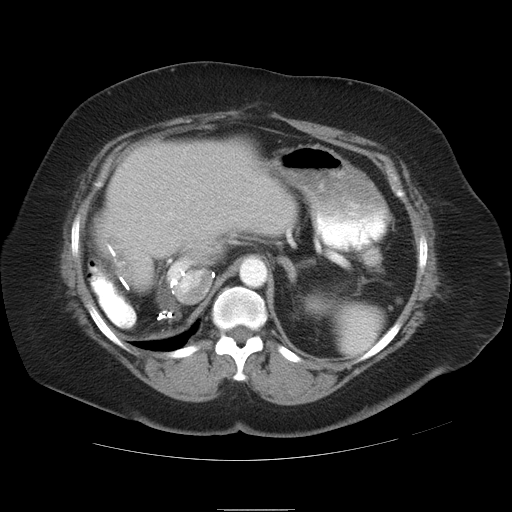
Contrast-enhanced abdominal CT, one axial slice. Position 23 of 37 along the scan axis. Soft-tissue window (W 400 / L 40 HU). 7.5 mm slice thickness. 512 × 512 image matrix, field of view 422 × 422 mm. Female patient, age 68 years. Case-level facts recorded for this patient, not image findings: diagnosis: colorectal cancer liver metastases, imaged before liver resection; multiple liver metastases: no; largest metastasis: 2 cm; chemotherapy before resection: no.
Annotated regions visible in this slice (manually delineated by an expert):
- liver: bounding box [x1, y1, x2, y2] px = [95, 138, 298, 289]
- planned liver remnant (the part of the liver to remain after resection): [106, 138, 299, 265]
- portal vein (with intrahepatic branches): [167, 219, 202, 294]
- liver metastasis: [100, 233, 135, 272]